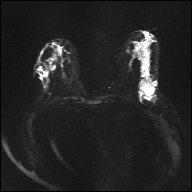
Breast MRI, one axial slice. Diffusion-weighted series; image 2 of 4 stored at this slice position (different b-values; order by instance number). 1.5 T. 192 × 192 image matrix, field of view 360 × 360 mm. Female patient.
Structures marked on this image (expert manual segmentation):
- tumour on diffusion-weighted imaging: bounding box [x1, y1, x2, y2] px = [139, 80, 154, 95]